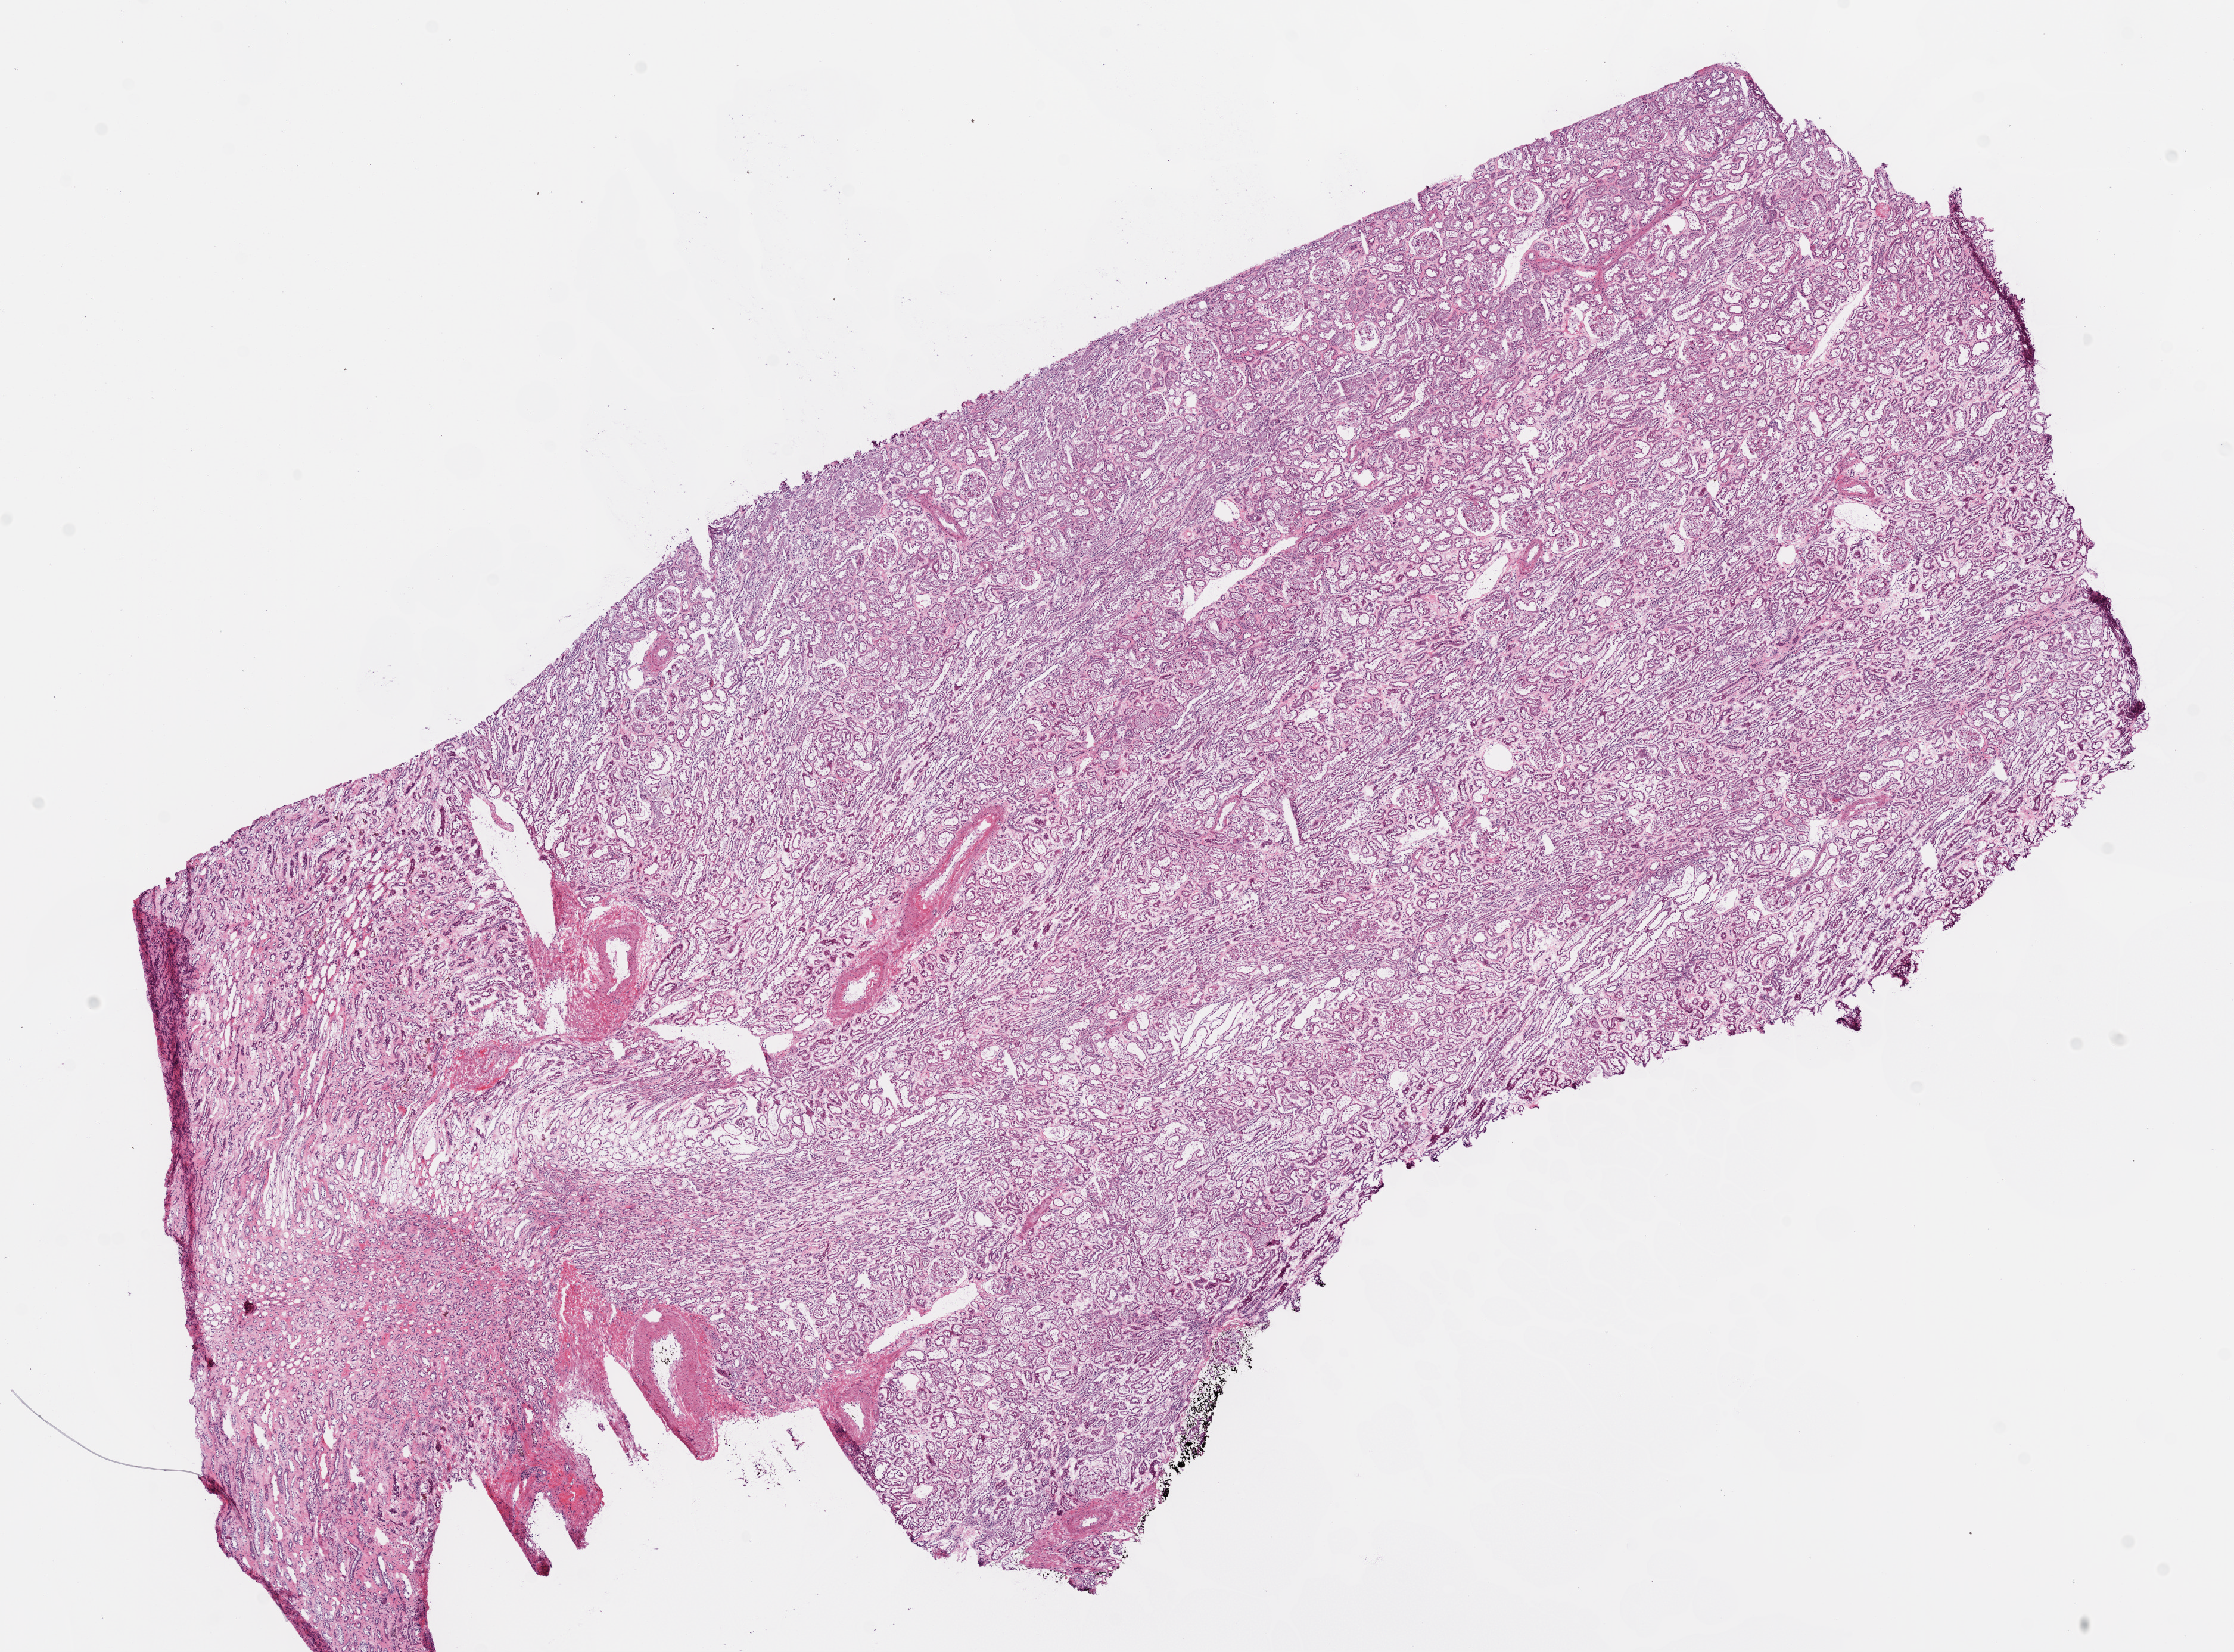
Whole-slide histology image, H&E-stained — low-resolution overview of the scanned area, about 15.0 x 11.1 mm; frozen section from the top of the tissue portion; solid tissue normal (non-tumour tissue) sample from the kidney. Patient: male, age at initial diagnosis 51 years.
This section: solid tissue normal (non-tumour) sample from the same patient. Patient diagnosis: Clear cell adenocarcinoma, NOS.